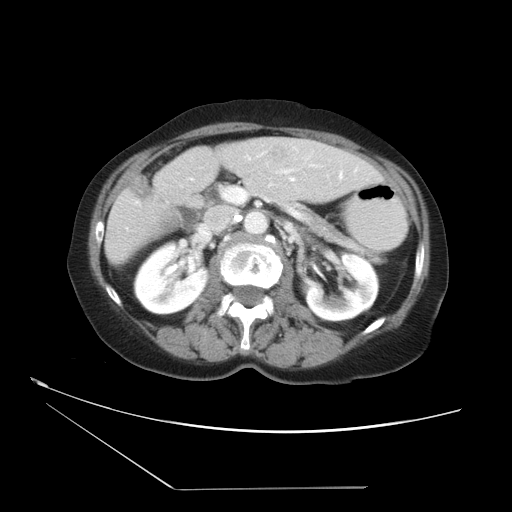
Contrast-enhanced abdominal CT, one axial slice; slice 15 of 36 in the series (ordered by position); 120 kVp; intravenous contrast given; soft-tissue window (W 400 / L 40 HU); 5 mm slice thickness; 512 × 512 image matrix, field of view 384 × 384 mm. Female patient, age 81 years. From the clinical record (not read from this slice): diagnosis: colorectal cancer liver metastases, imaged before liver resection.
Structures marked on this image (expert manual segmentation):
- hepatic veins: bounding box [x1, y1, x2, y2] px = [292, 174, 342, 181]
- liver: [105, 138, 382, 265]
- planned liver remnant (the part of the liver to remain after resection): [105, 146, 382, 265]
- portal vein (with intrahepatic branches): [226, 189, 243, 202]
- liver metastasis: [267, 142, 294, 163]